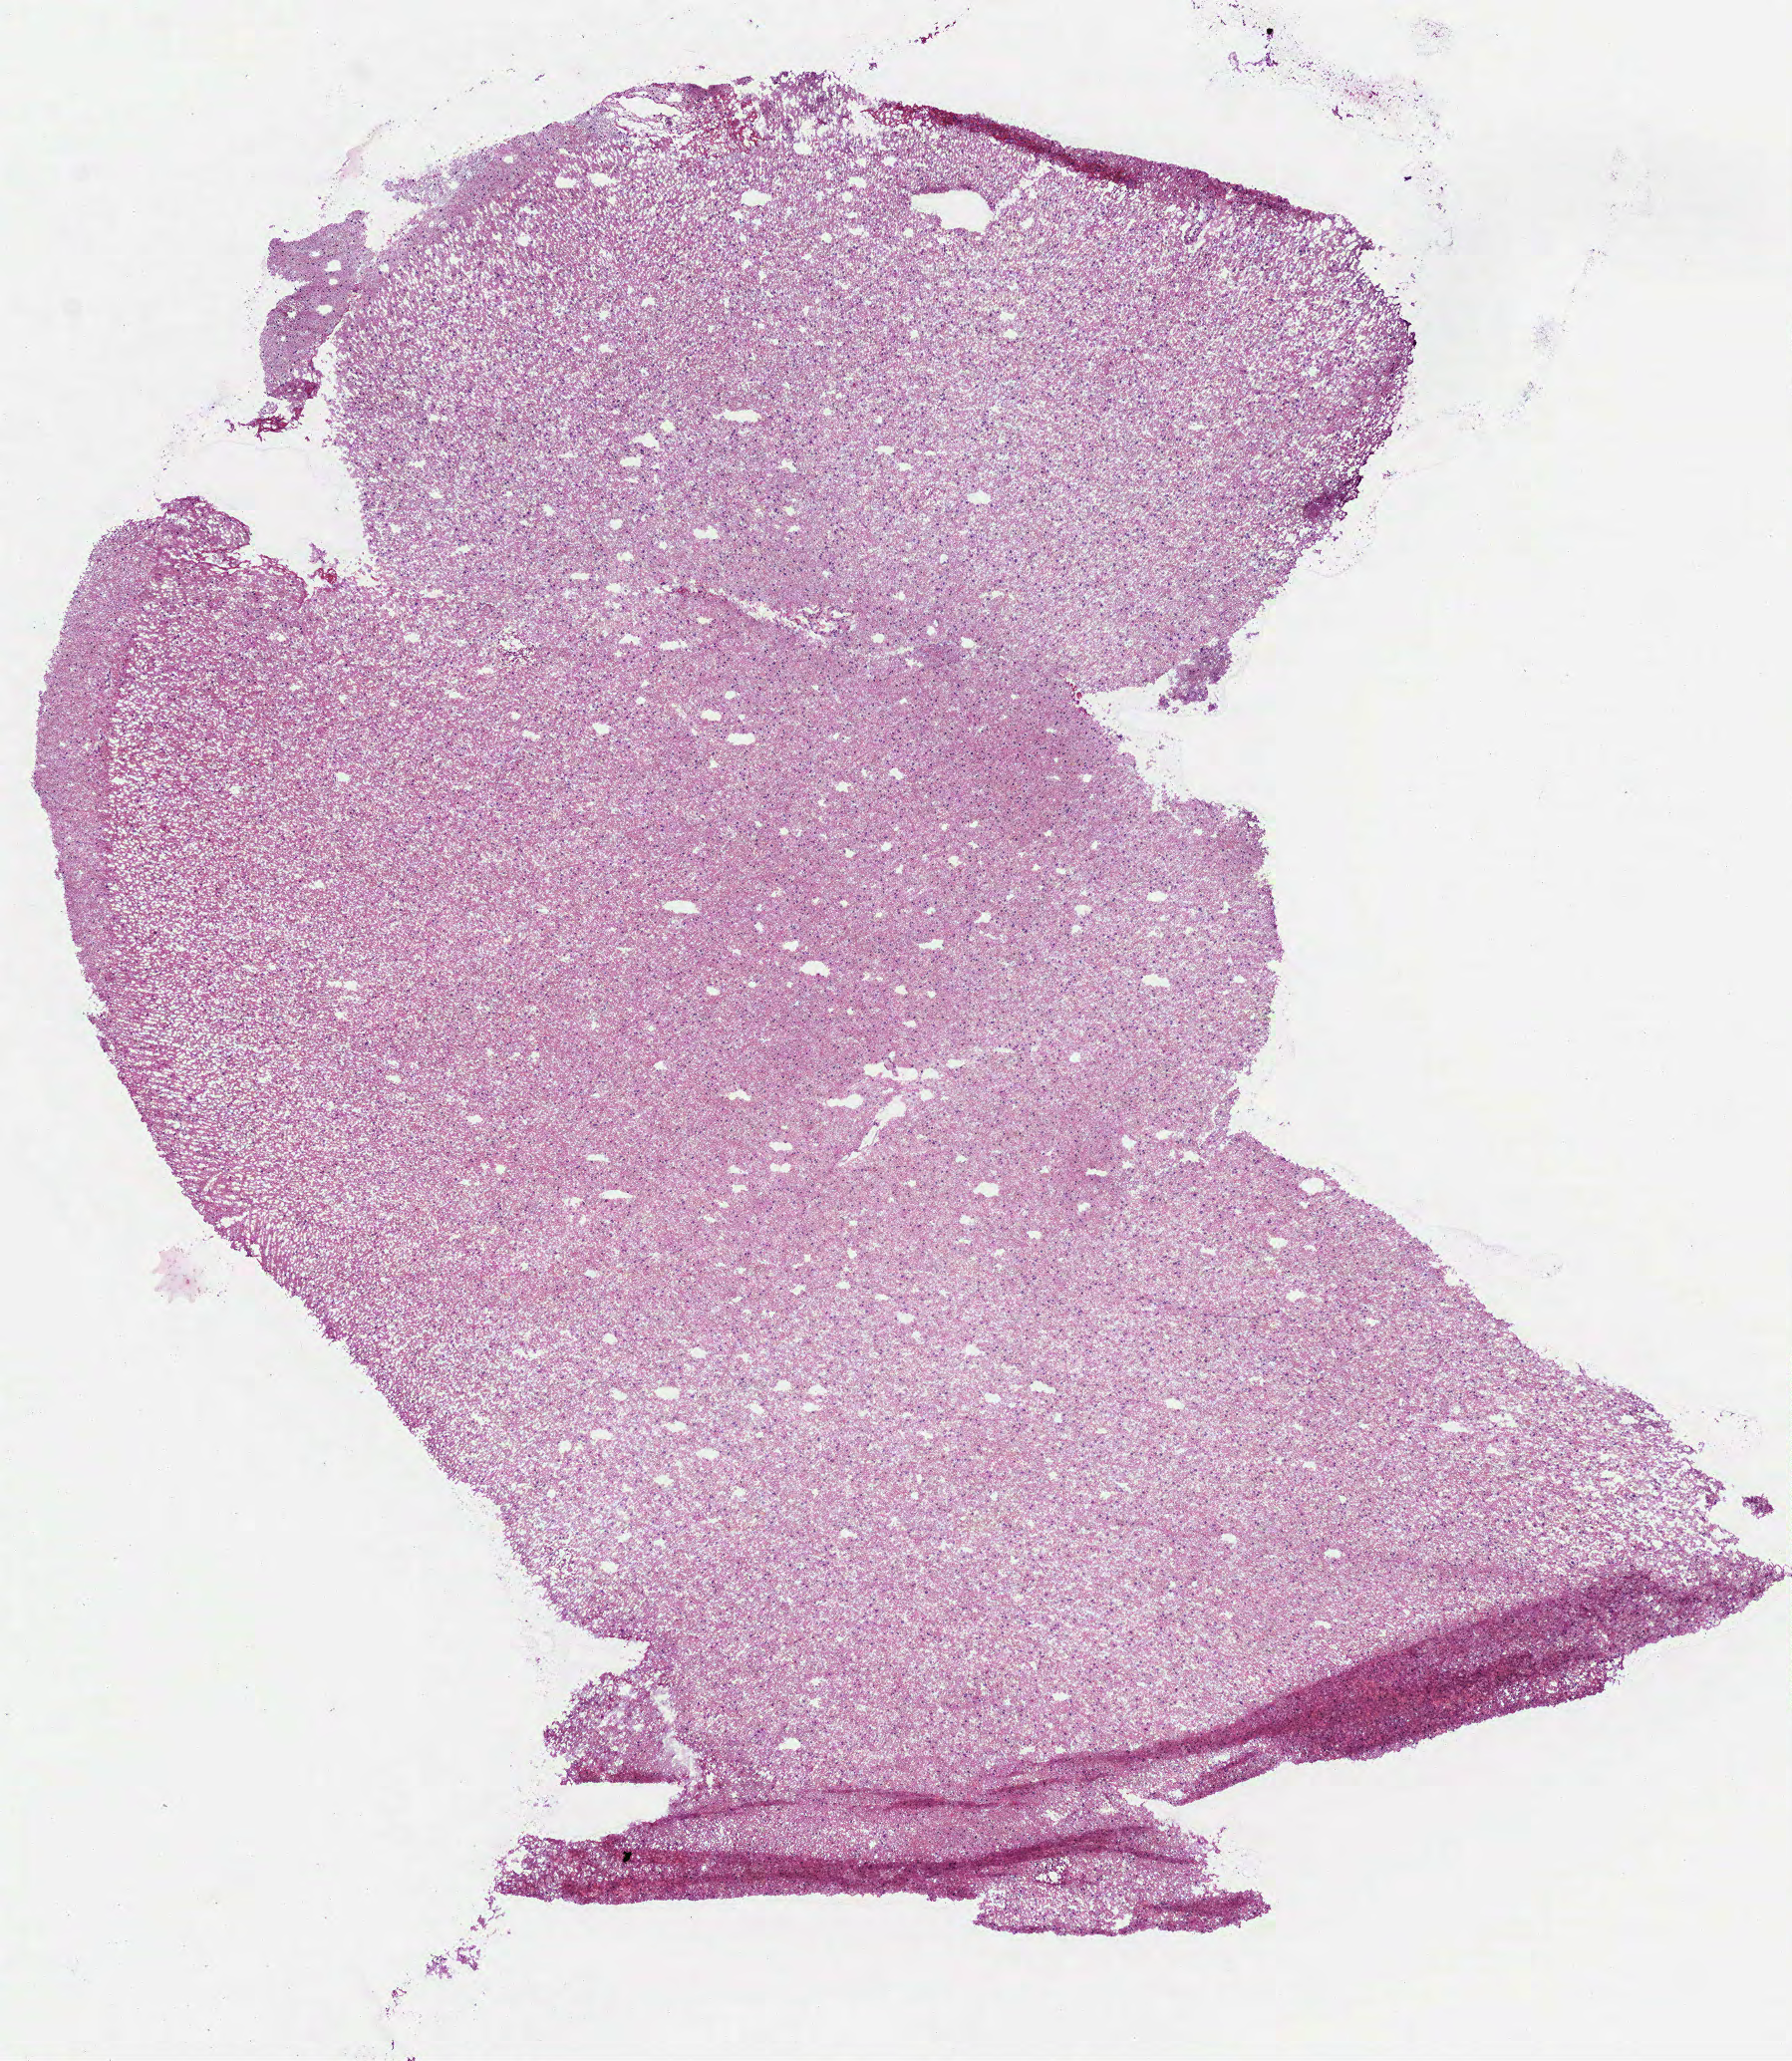
Digitized Hematoxylin and eosin (H&E) stained tissue section (whole slide), a low-resolution overview of the entire scanned area, about 7.3 x 8.3 mm (slide scanned at 40x); frozen section; sample: primary tumour, brain. Female patient; age at initial diagnosis 18 years. Histologic grade: G2 (moderately differentiated). Pathologist review of this section (percent, as recorded): tumour cells 100%, tumour nuclei 70%, normal cells 0%, stromal cells 0%, necrosis 0%.
• diagnosis: Mixed glioma